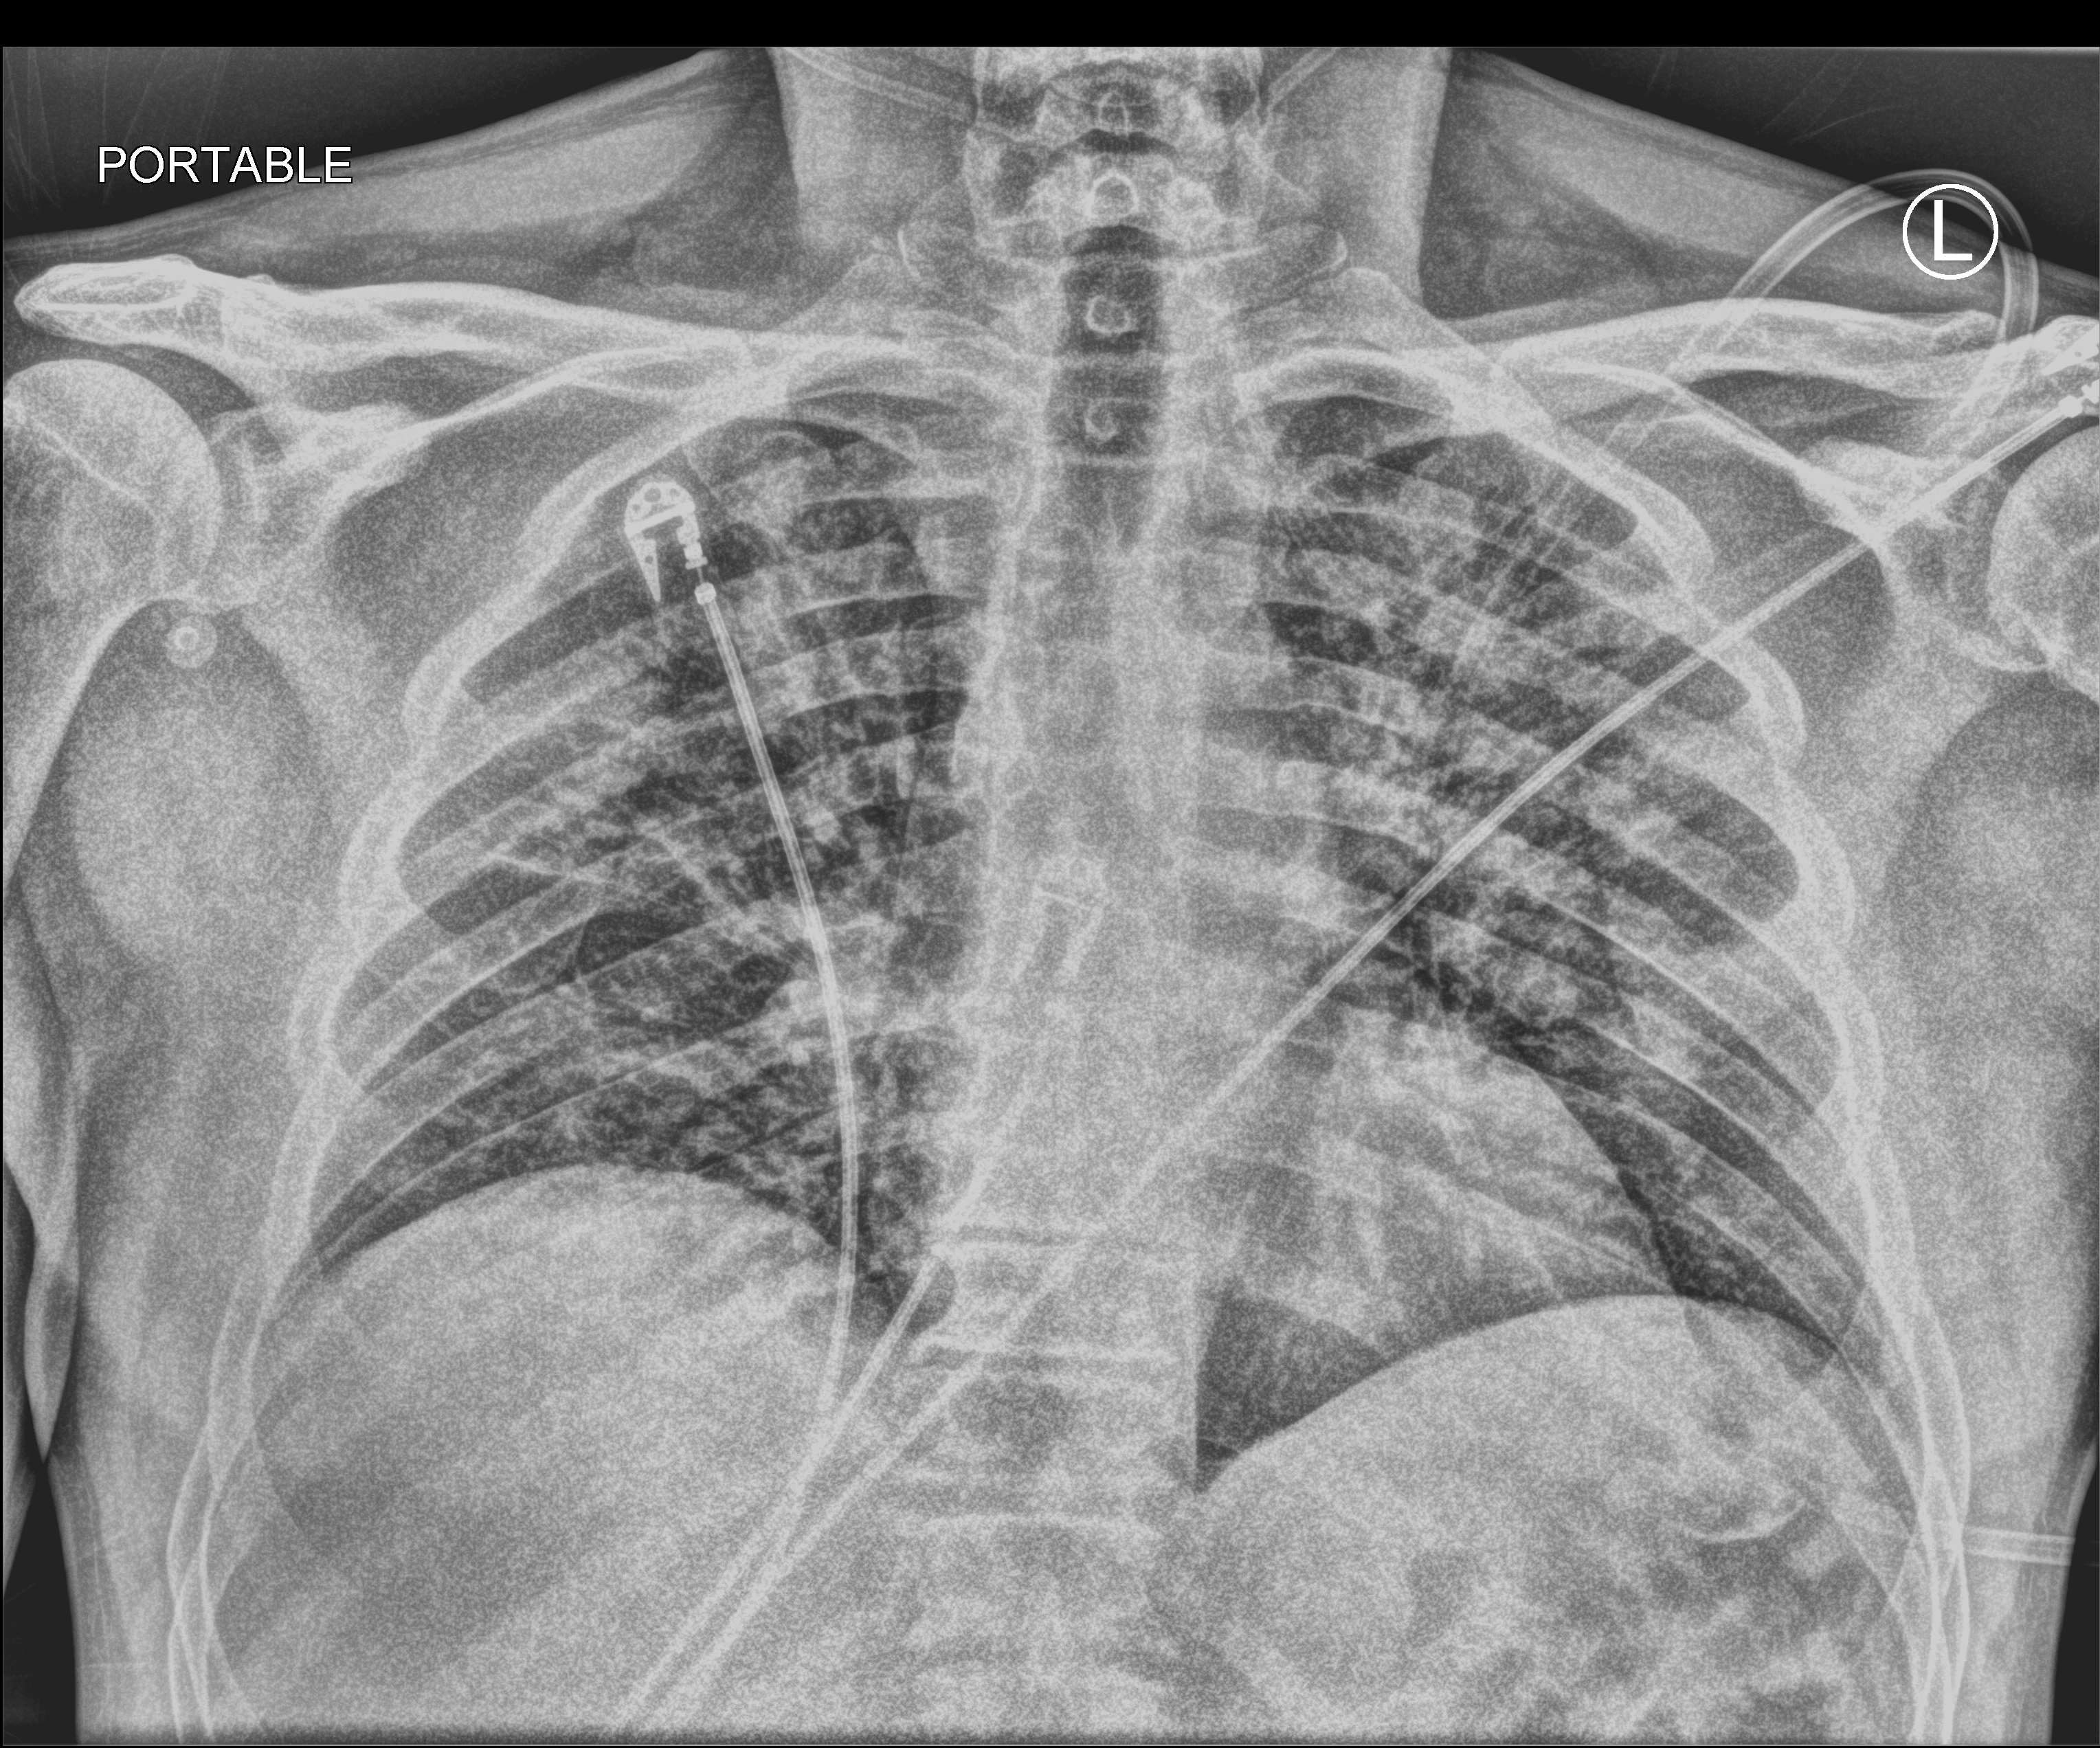
Portable chest radiograph. Patient hospitalised with COVID-19; male, aged 18–59 years.
From the hospital-stay record, not from the radiograph (when in the stay this image was taken is not recorded):
- chronic kidney disease (admission record): no